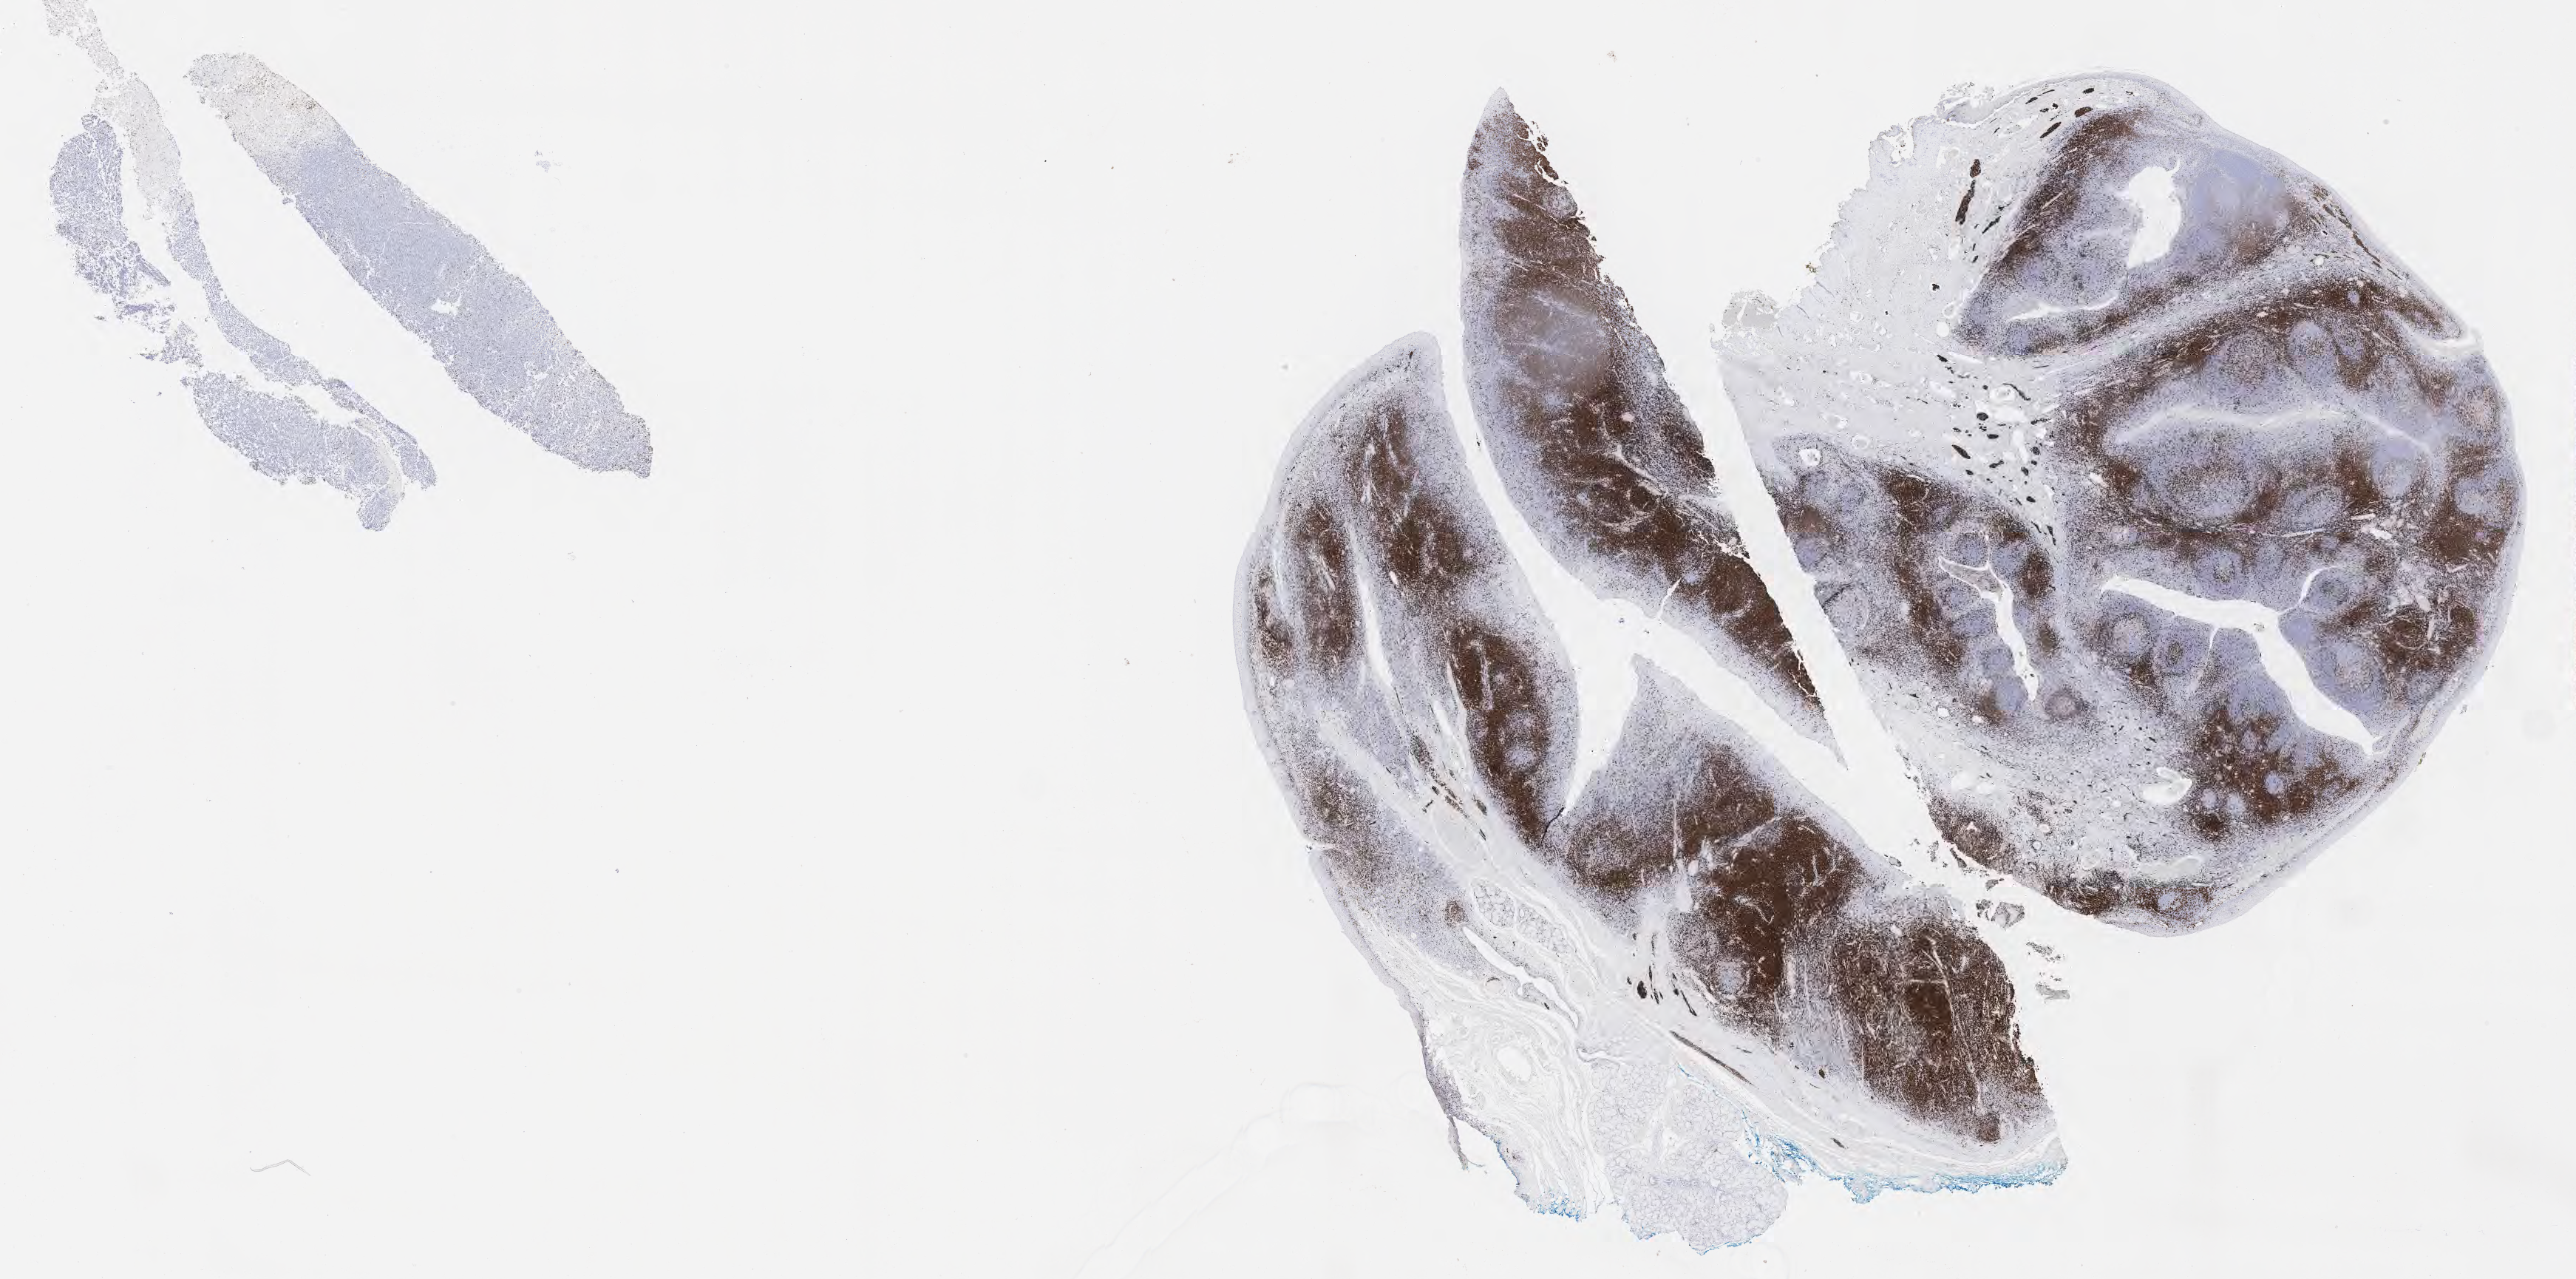
IHC for CD3, whole-slide image, a low-resolution overview of the entire scanned area, about 28.2 x 14.0 mm, tumor tissue. Patient: female, 18 years old.
Diagnosis: Burkitt lymphoma, NOS.